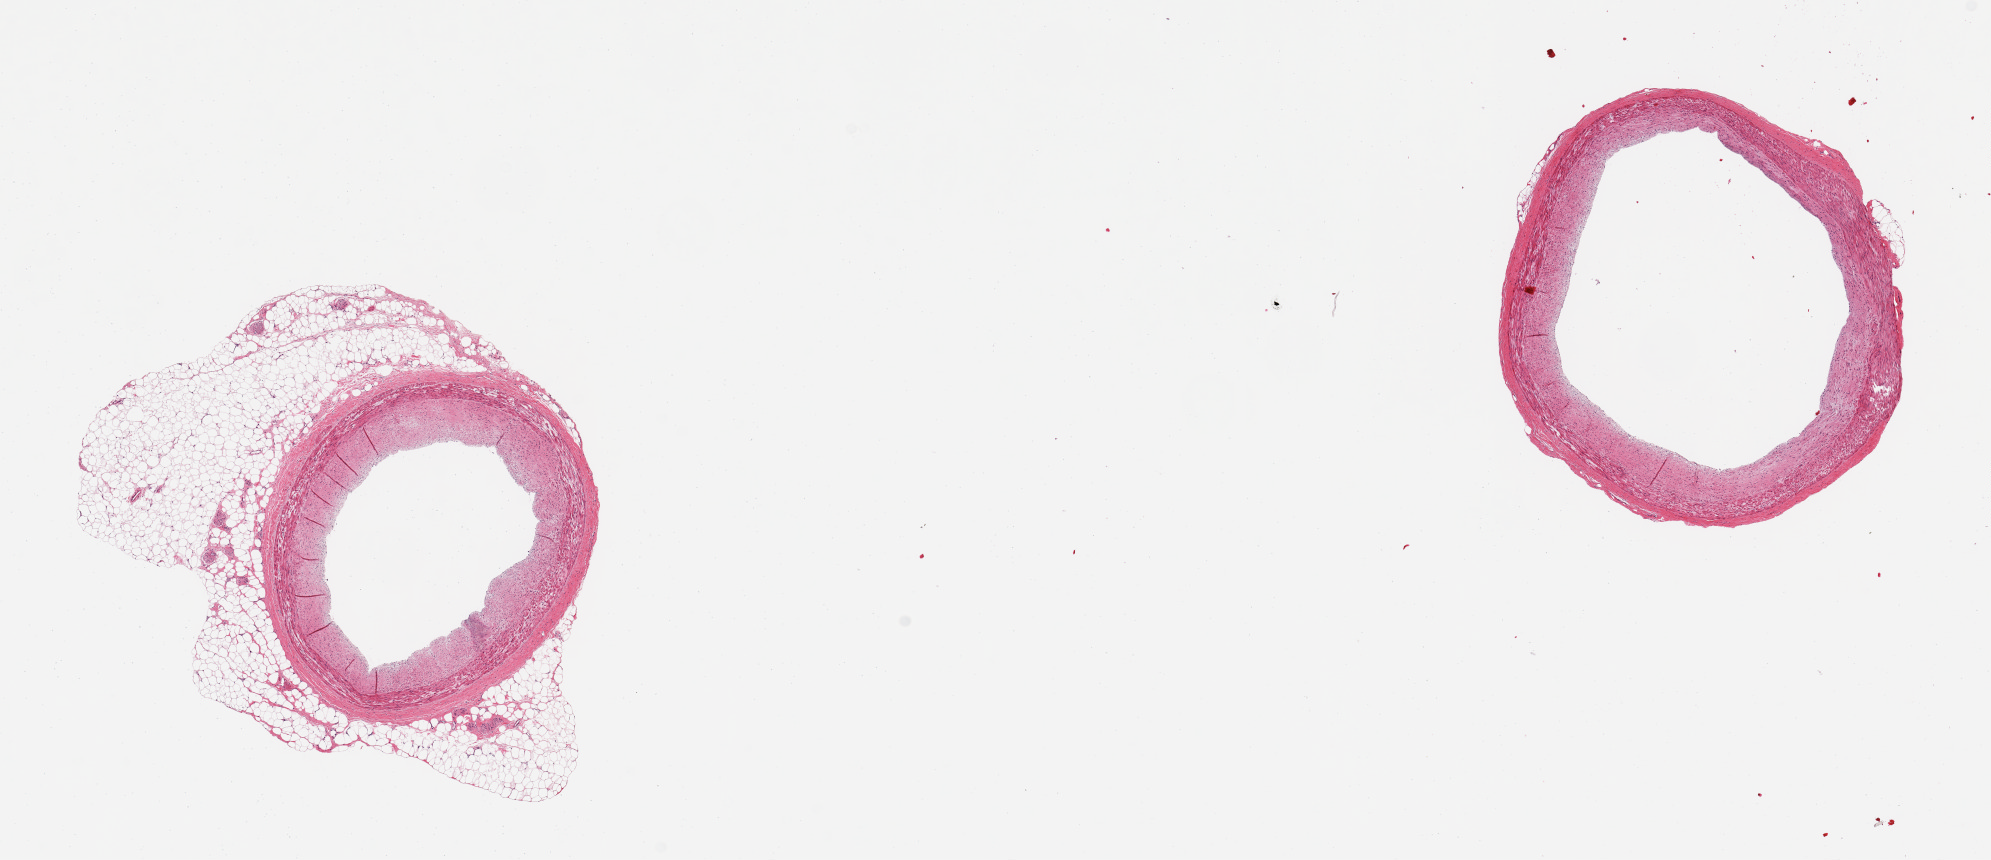
Whole-slide image, hematoxylin and eosin (H&E) stain — whole scanned area (about 15.8 x 6.8 mm) shown as a low-resolution overview; PAXgene-fixed, paraffin-embedded tissue; sampled site (target tissue): coronary artery; donor tissue sample. Donor sex: male.
Reviewer comment on this tissue sample: 2 pieces; one well trimmed; other with 1.5mm adherent fat.